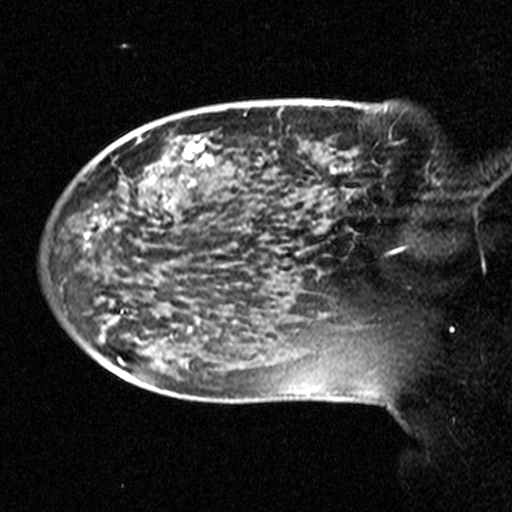
Breast MRI (dynamic contrast-enhanced), one sagittal slice. Slice 11 of 44 in the series (ordered by position). Dynamic contrast-enhanced study with each time point stored as its own series, time point 2 of 3 at this slice position (early post-contrast, ordered by acquisition time). 1.5 T. TE 4.5 ms, TR 11 ms. 3 mm slice thickness. 512 × 512 image matrix, field of view 240 × 240 mm. Female patient, age 38 years. Case-level facts recorded for this patient, not image findings: setting: breast cancer imaged before/during neoadjuvant chemotherapy; receptor status: HR-positive, HER2-negative.
Outlined on this slice (semi-automatically segmented with operator editing):
- analysis volume of interest (the breast-tissue region the enhancement analysis was run in; not a lesion): bounding box <124,106,405,245> (left, top, right, bottom; pixels)
- tumour enhancement mask (voxels above the 90 % enhancement threshold inside the analysis volume of interest): <153,143,394,180>